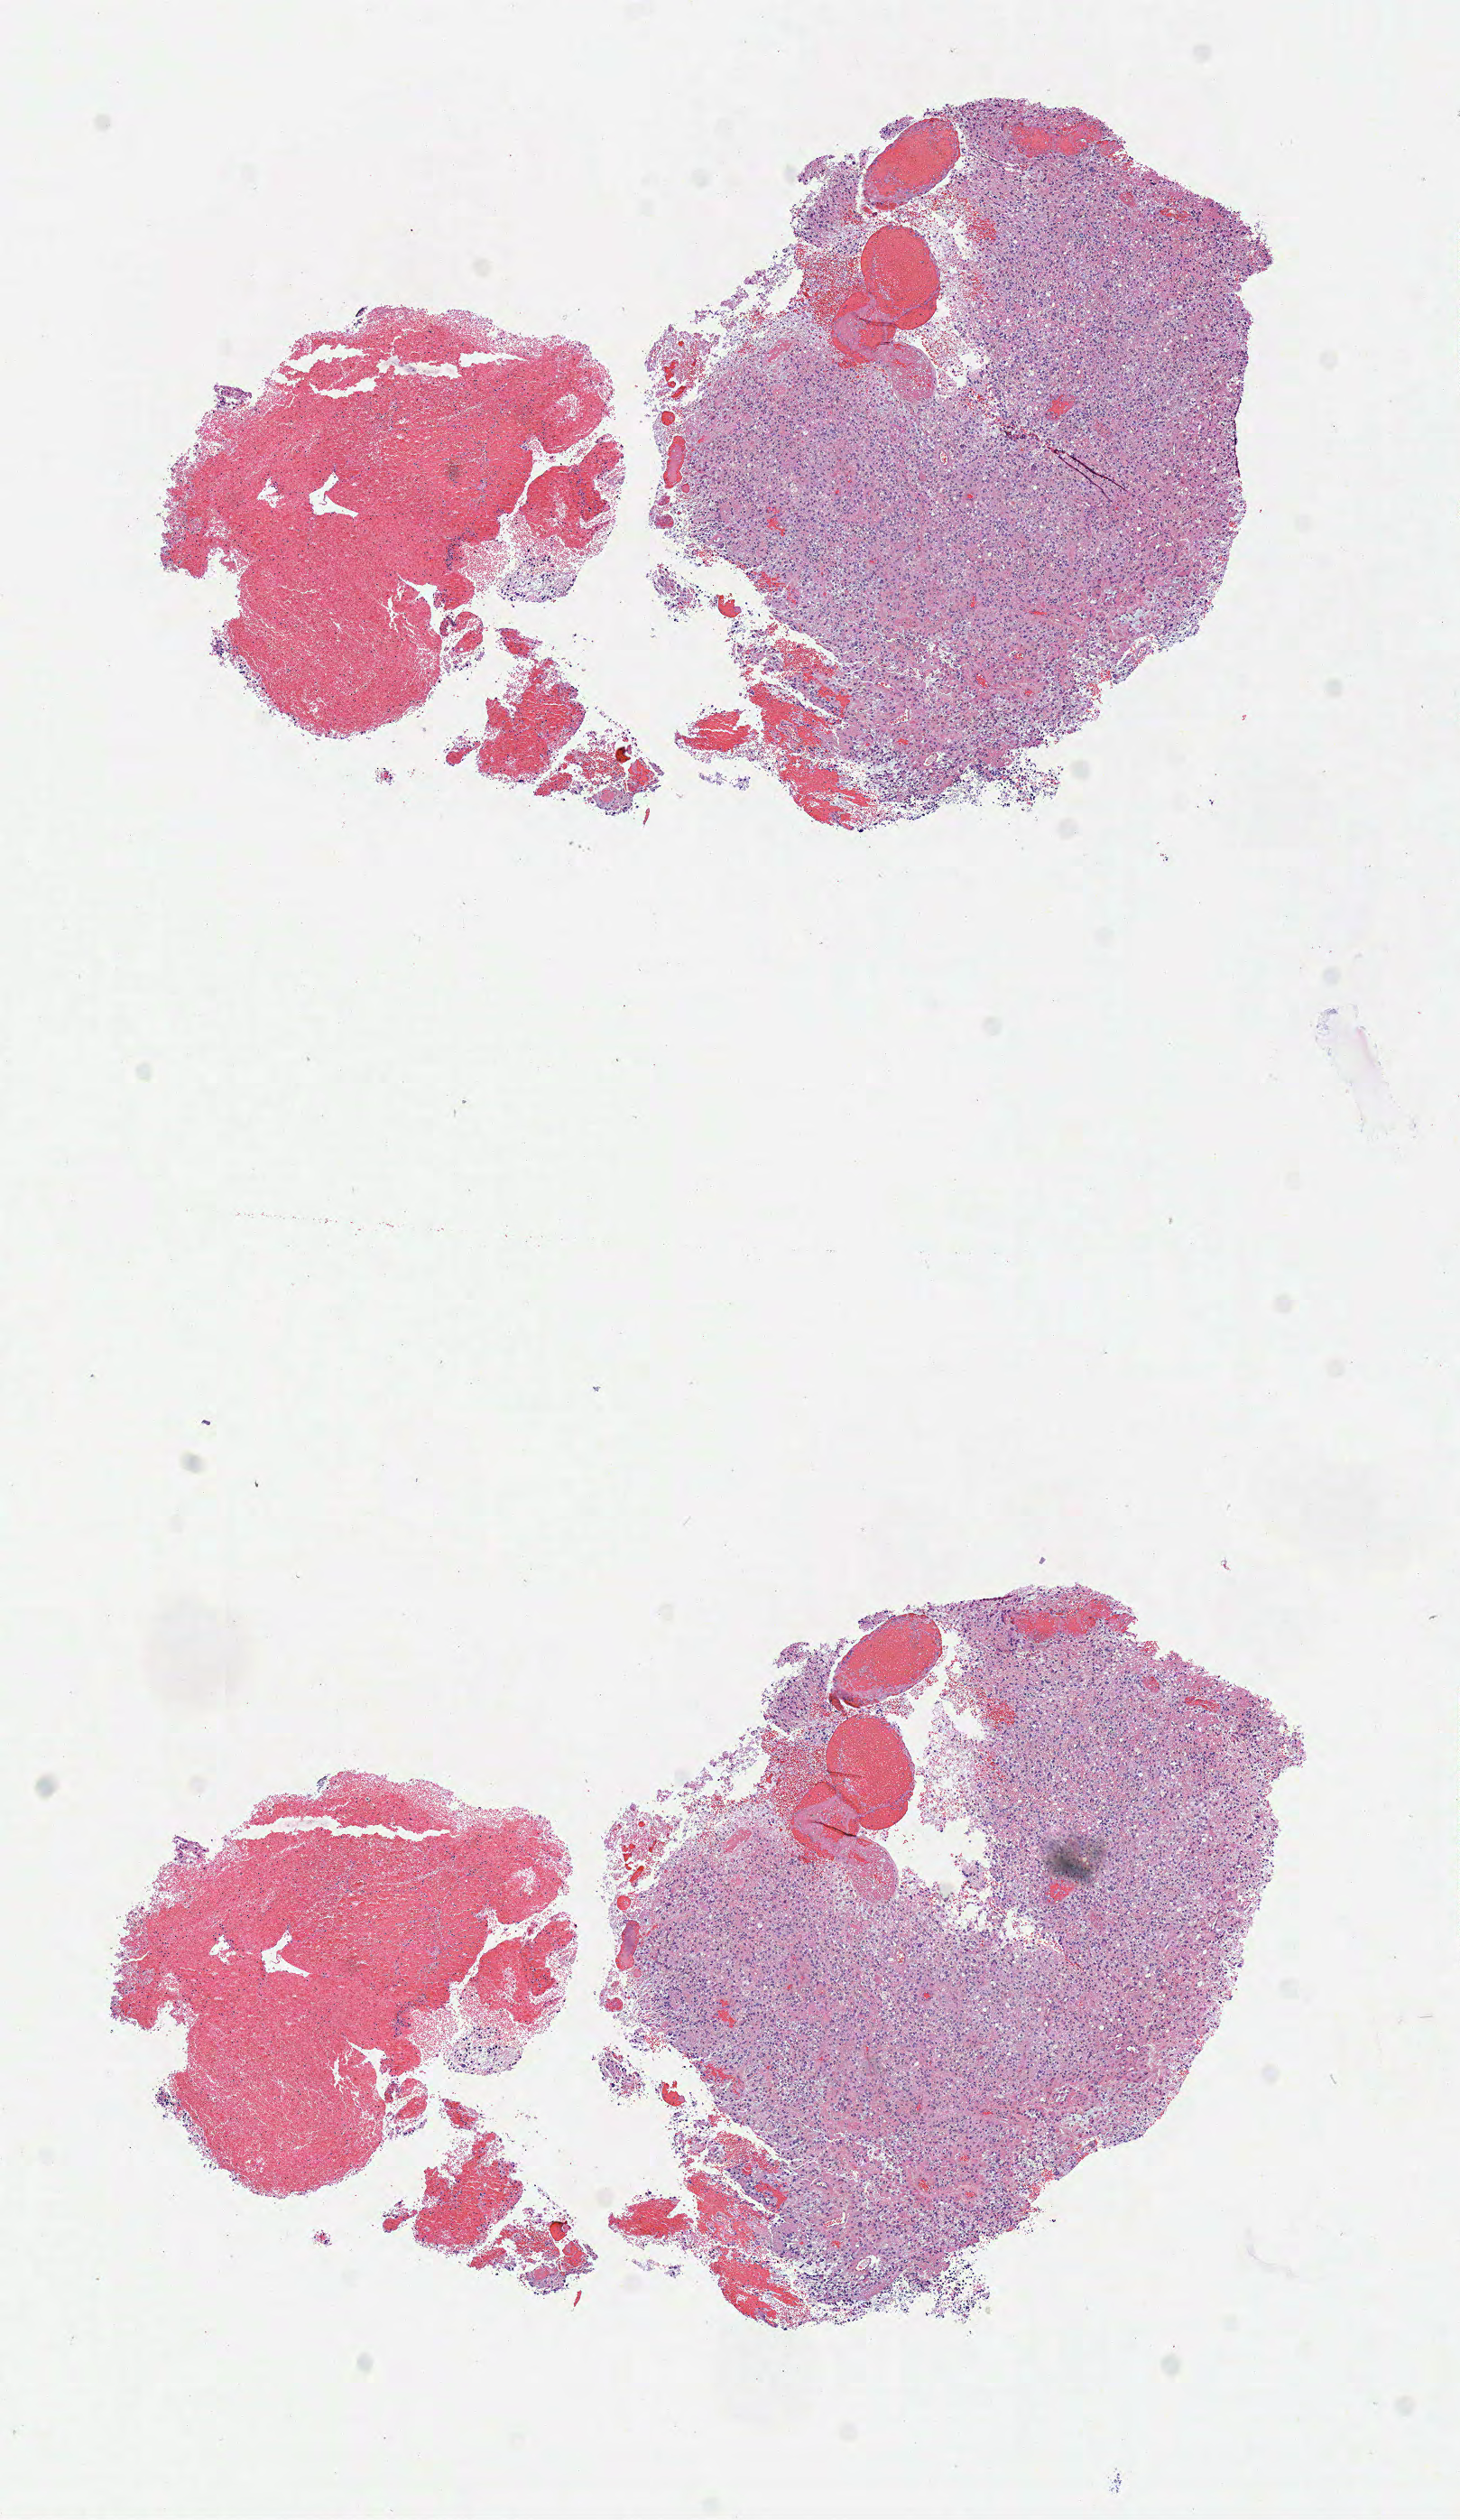
Digitized H&E tissue section (whole slide), shown as a low-resolution overview of the whole scanned area (about 6.4 x 11.0 mm, from a 40x scan); frozen section from the top of the tissue portion; sample: primary tumour, brain. Male, age 58 years at initial diagnosis. Composition of this section per pathologist review: tumour cells 97%, tumour nuclei 85%, normal cells 0%, stromal cells 5%, necrosis 3%.
• pathologic diagnosis: Glioblastoma